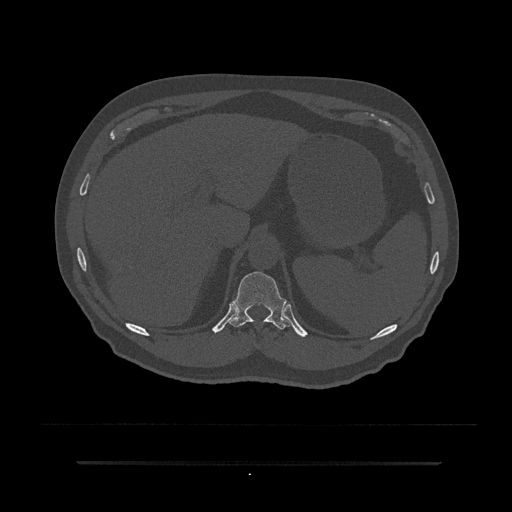
CT including the spine, one axial slice; reconstruction kernel Br40s/3; 120 kVp; bone window (W 1800 / L 400 HU); 0.5 mm slice thickness; 512 × 512 image matrix, field of view 464 × 464 mm. Patient: male, 59 years. From the clinical record (not read from this slice): primary cancer: bile ducts.
Annotated regions visible in this slice (semi-automatic segmentation, software-assisted and operator-edited):
- T11 vertebra: box from (x=230, y=271) to (x=293, y=329) px